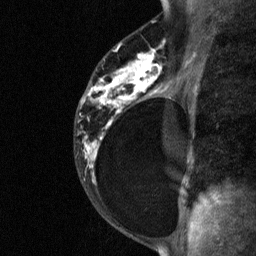
Breast MRI (dynamic contrast-enhanced), one sagittal slice; dynamic contrast-enhanced study with each time point stored as its own series, time point 2 of 3 at this slice position (early post-contrast, ordered by acquisition time); 1.5 T; TE 4.8 ms, TR 27 ms; 2 mm slice thickness; 256 × 256 image matrix, field of view 180 × 180 mm. Female patient, age 34 years. Case-level facts recorded for this patient, not image findings: setting: breast cancer imaged before/during neoadjuvant chemotherapy; receptor status: HR-positive, HER2-negative.
Structures marked on this image (semi-automatic segmentation, software-assisted and operator-edited):
- analysis volume of interest (the breast-tissue region the enhancement analysis was run in; not a lesion): bounding box (x1, y1, x2, y2) in pixels: (78, 44, 181, 191)
- tumour enhancement mask (voxels above the 90 % enhancement threshold inside the analysis volume of interest): (82, 50, 161, 167)